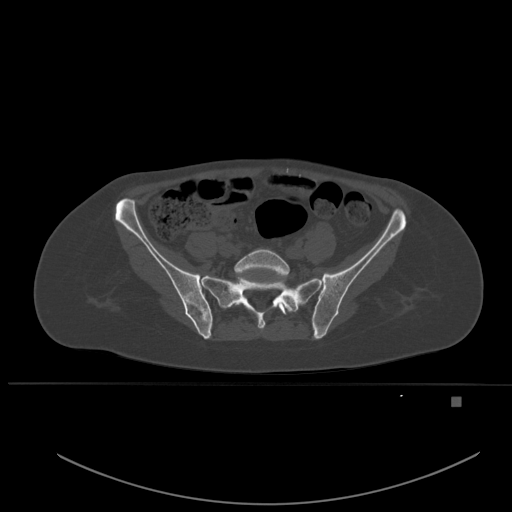
CT including the spine, one axial slice; bone window (W 1800 / L 400 HU); 1.5 mm slice thickness; 512 × 512 image matrix, field of view 443 × 443 mm. Patient: female, 49 years. Case-level facts recorded for this patient, not image findings: primary cancer: breast; vertebrae with lytic lesions (as recorded): L3, T12, L4.
Structures marked on this image (semi-automatic segmentation, software-assisted and operator-edited):
- L5 vertebra: box from (x=234, y=249) to (x=292, y=315) px